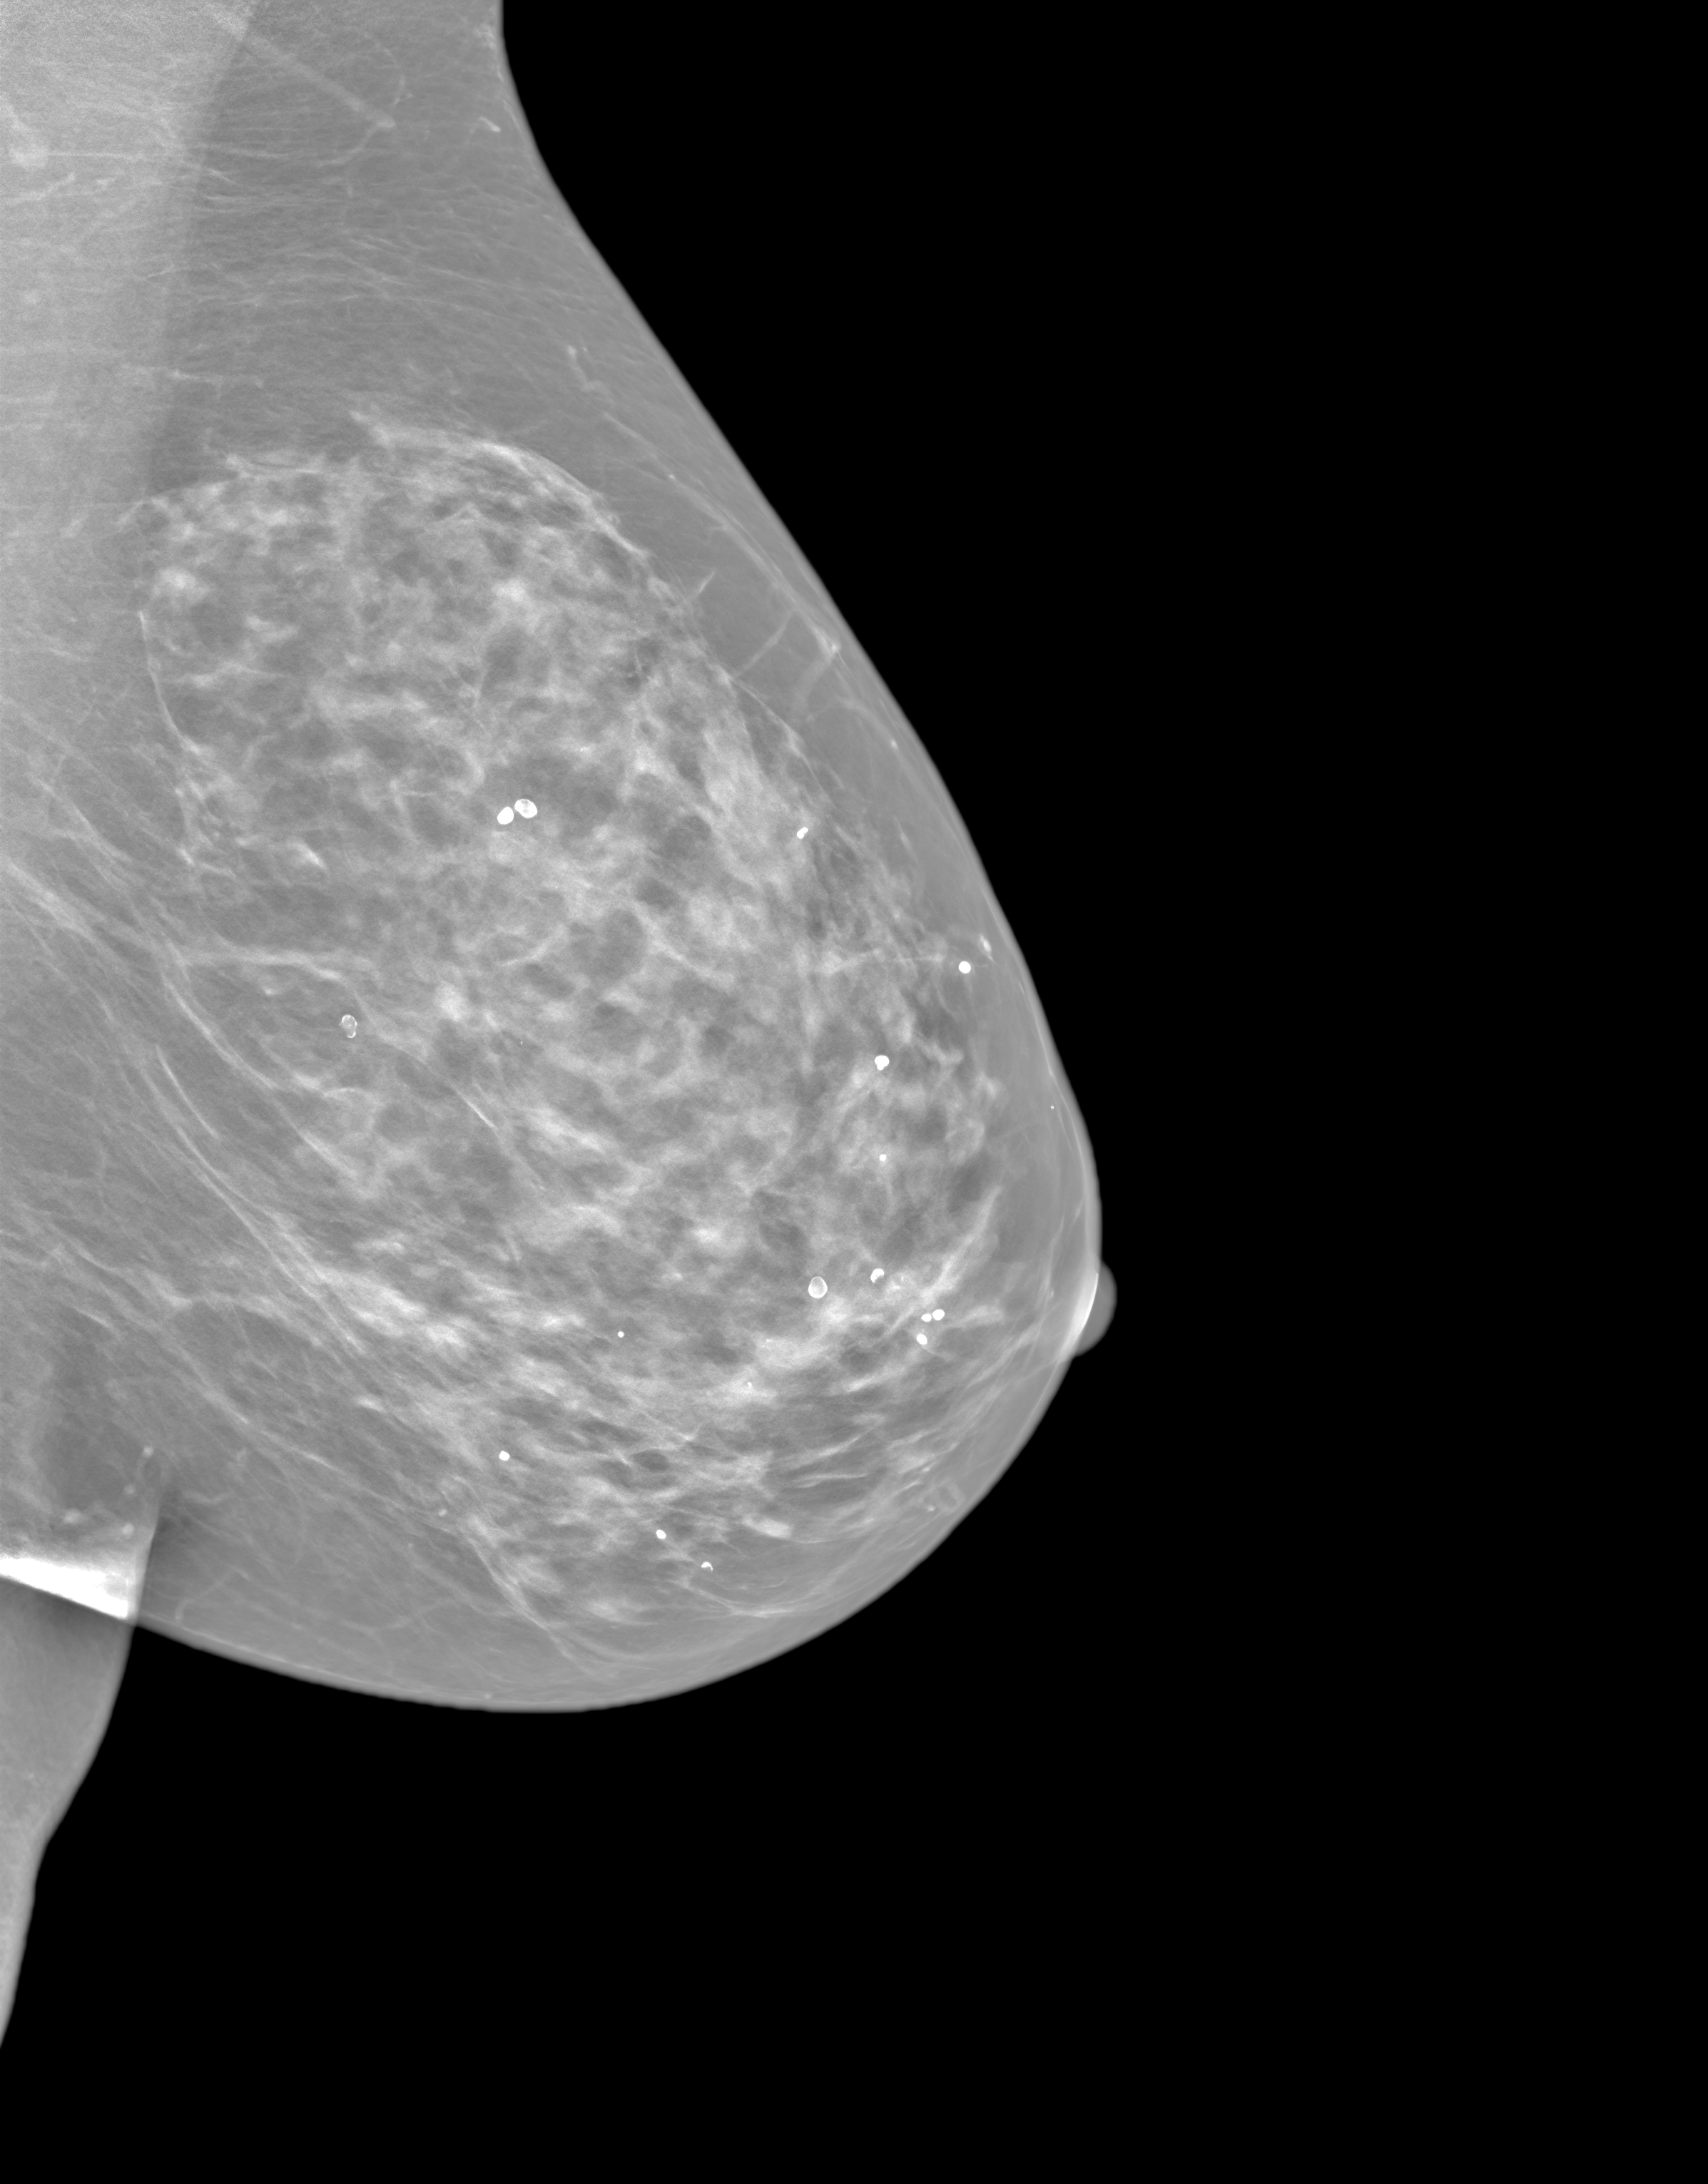
Synthesized 2-D mammogram reconstructed from digital breast tomosynthesis; left breast; MLO view; annual screening mammography examination. Patient: female, 66 years.
- BI-RADS breast density category at the screening exam (both breasts, scale 1–4): 3
- final BI-RADS category for the screening round (tomosynthesis exam, both breasts): category 1
- recall: no recall after this screen